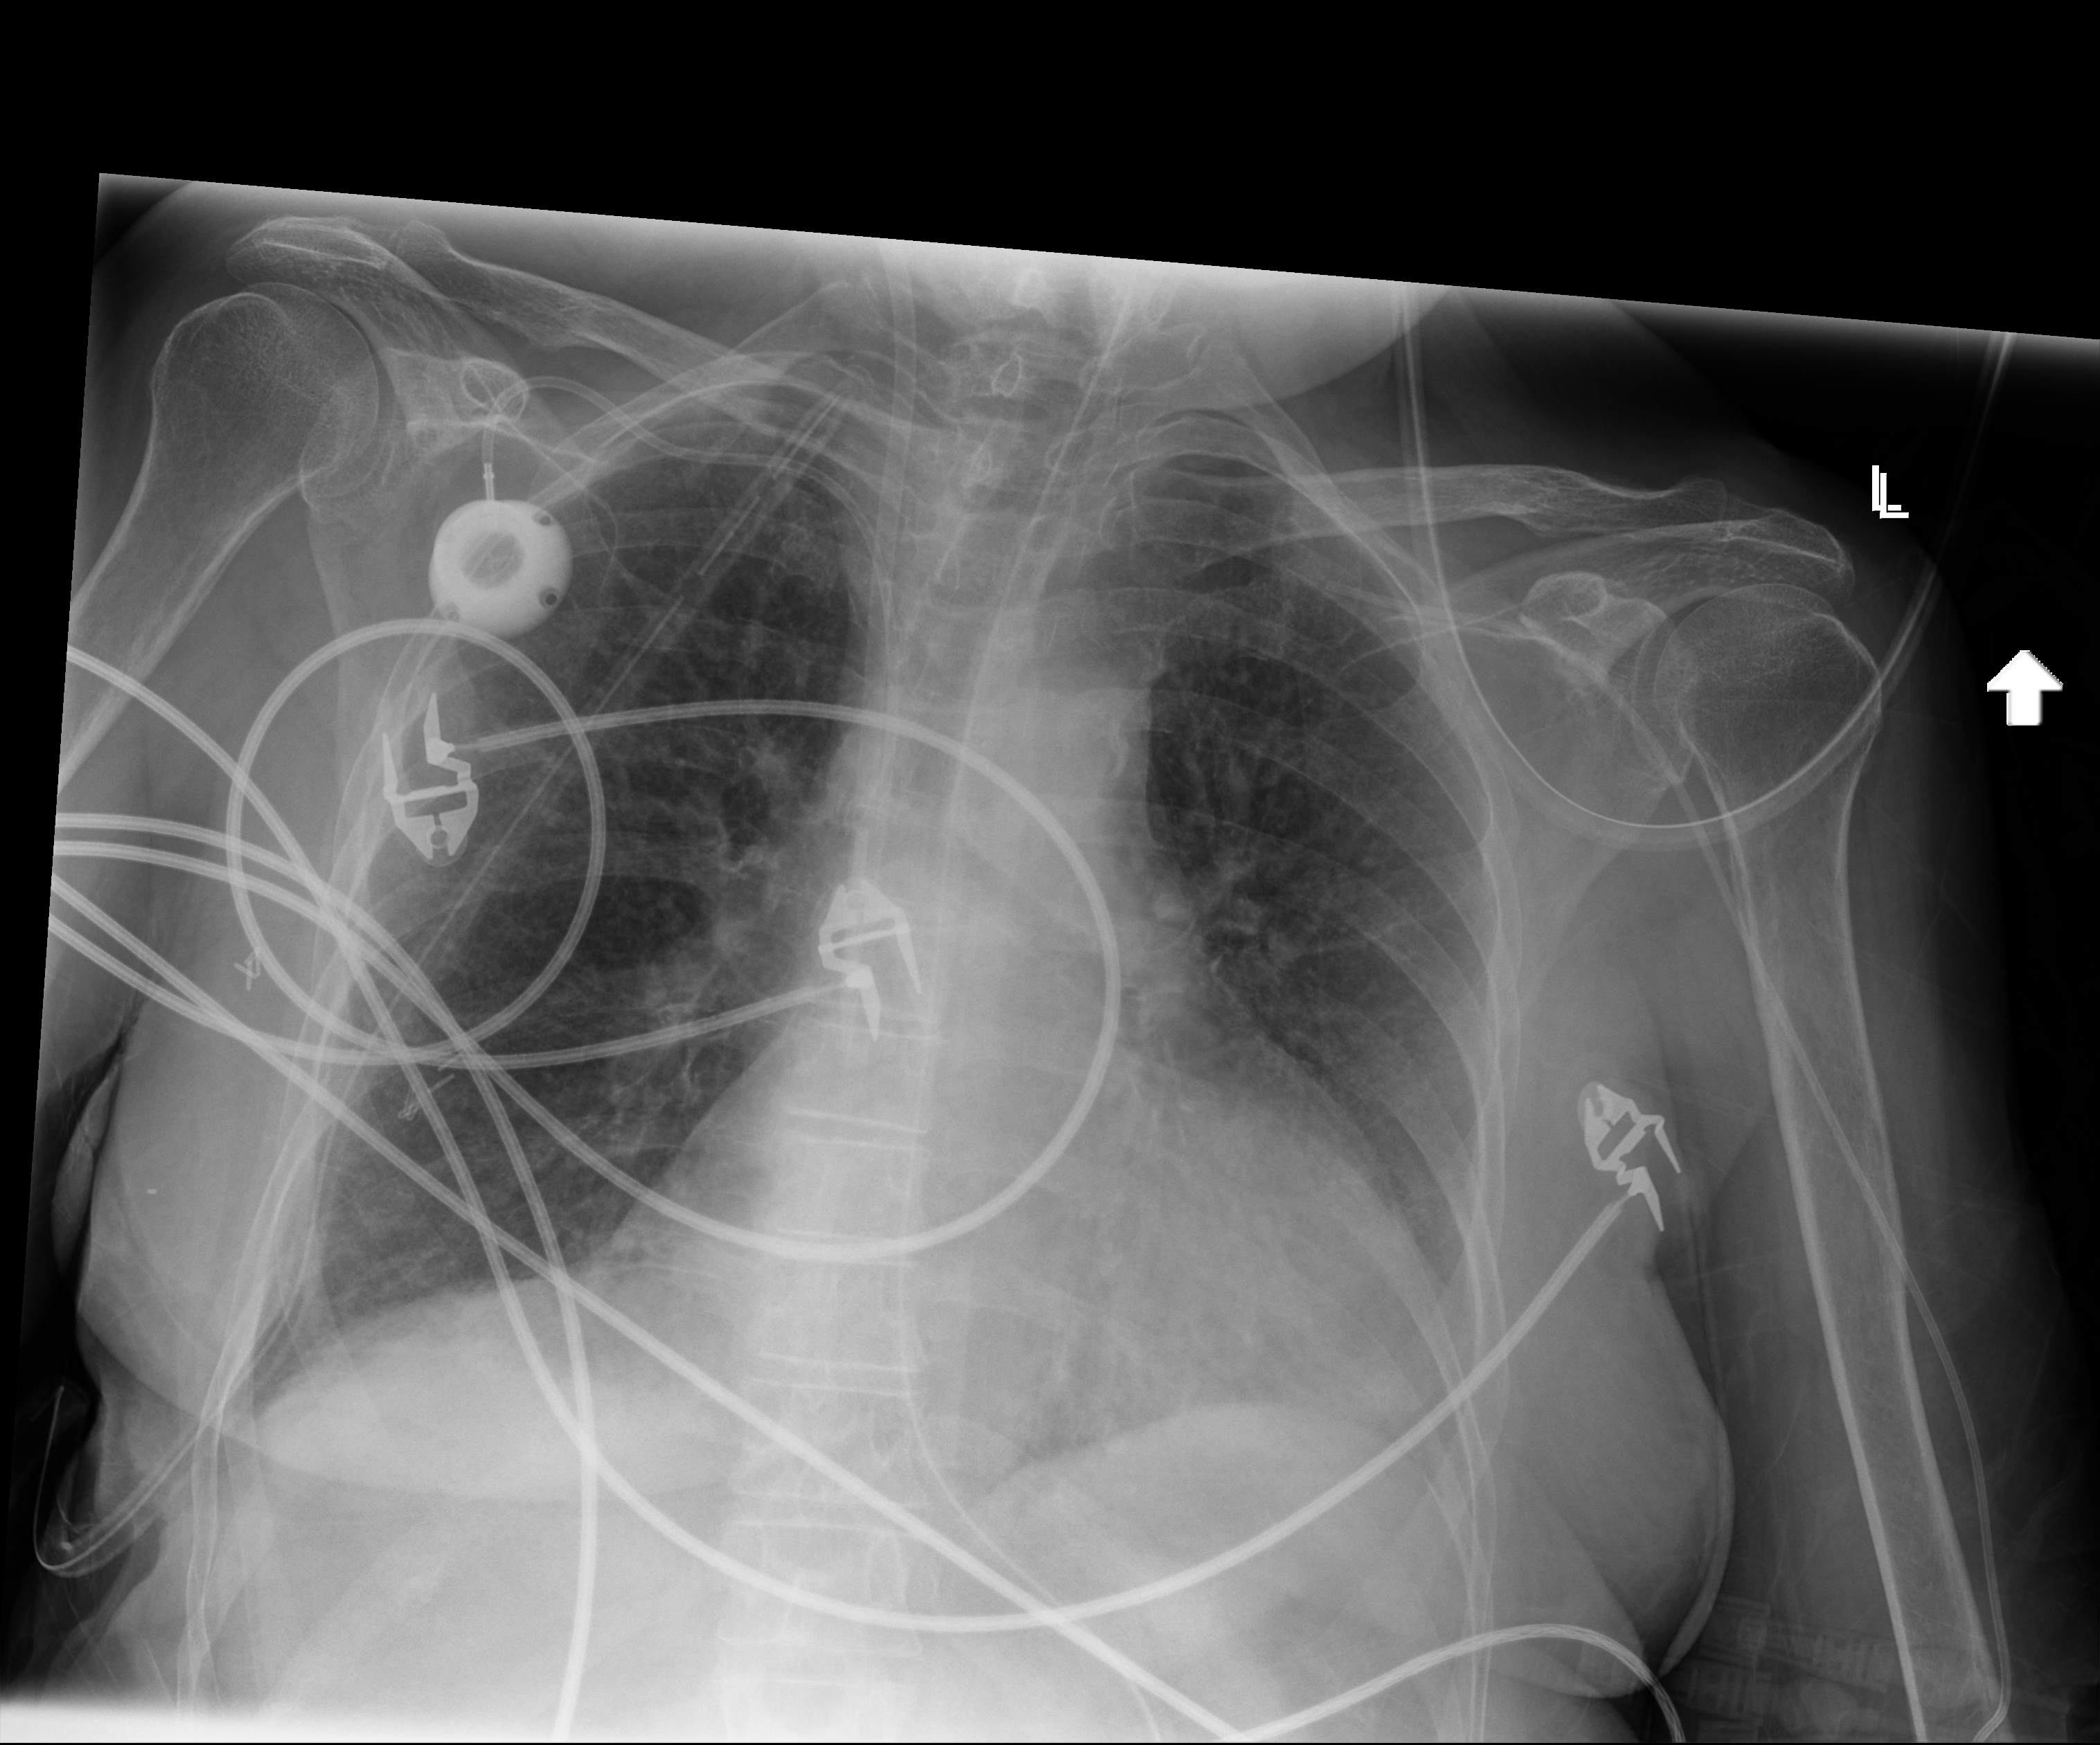
Chest X-ray, anteroposterior (AP) projection. Patient hospitalised with COVID-19; female, aged 60–74 years.
Admission-level facts for this patient (not findings on this image; timing relative to this image not recorded):
- mechanically ventilated during this hospital stay: yes
- admitted to intensive care during this hospital stay: yes
- length of hospital stay: 43 days